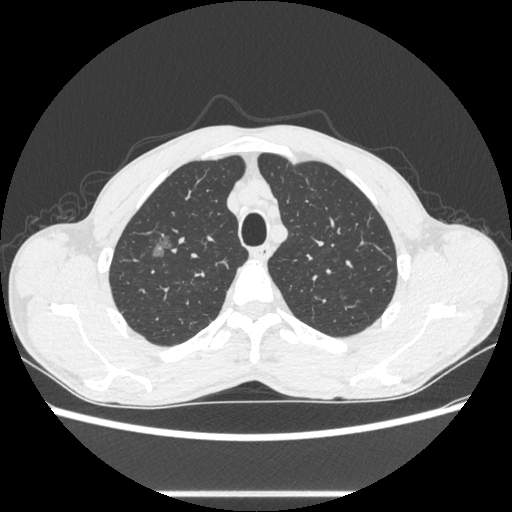
Chest CT, one axial slice. Position 479 of 600 along the scan axis. Reconstruction kernel STANDARD. 100 kVp. Lung window (W 1500 / L -600 HU). 512 × 512 image matrix, field of view 357 × 357 mm. Male patient, age 54 years. Case-level facts recorded for this patient, not image findings: clinical TNM (as recorded): T1a N0 M0.
Outlined on this slice (rectangle marked by the reading radiologist):
- lung tumour (recorded histology: adenocarcinoma): bounding box [x1, y1, x2, y2] px = [145, 226, 179, 262]